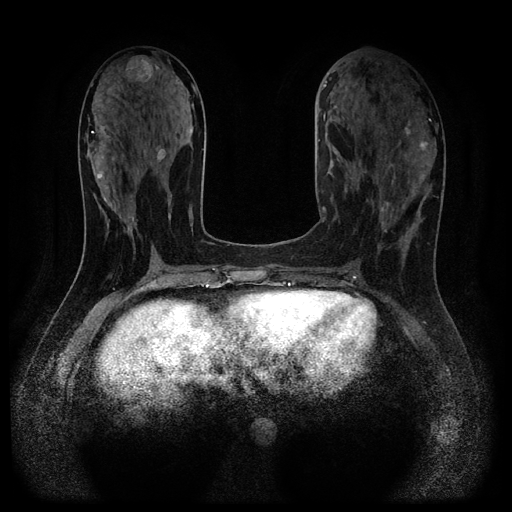
Breast MRI (dynamic contrast-enhanced, multi-phase), one axial slice. Position 47 of 116 along the scan axis. Dynamic contrast-enhanced series, time point 2 of 5 at this slice position (early post-contrast). 1.5 T. TE 2.7 ms, TR 5.4 ms. 2.2 mm slice thickness. 512 × 512 image matrix. Female patient, age 43 years.
Annotated regions visible in this slice (semi-automatically segmented with operator editing):
- breast lesion (labelled benign in the annotation): bounding box <156,146,166,162> (left, top, right, bottom; pixels)
- breast lesion (labelled benign in the annotation): <124,55,157,83>